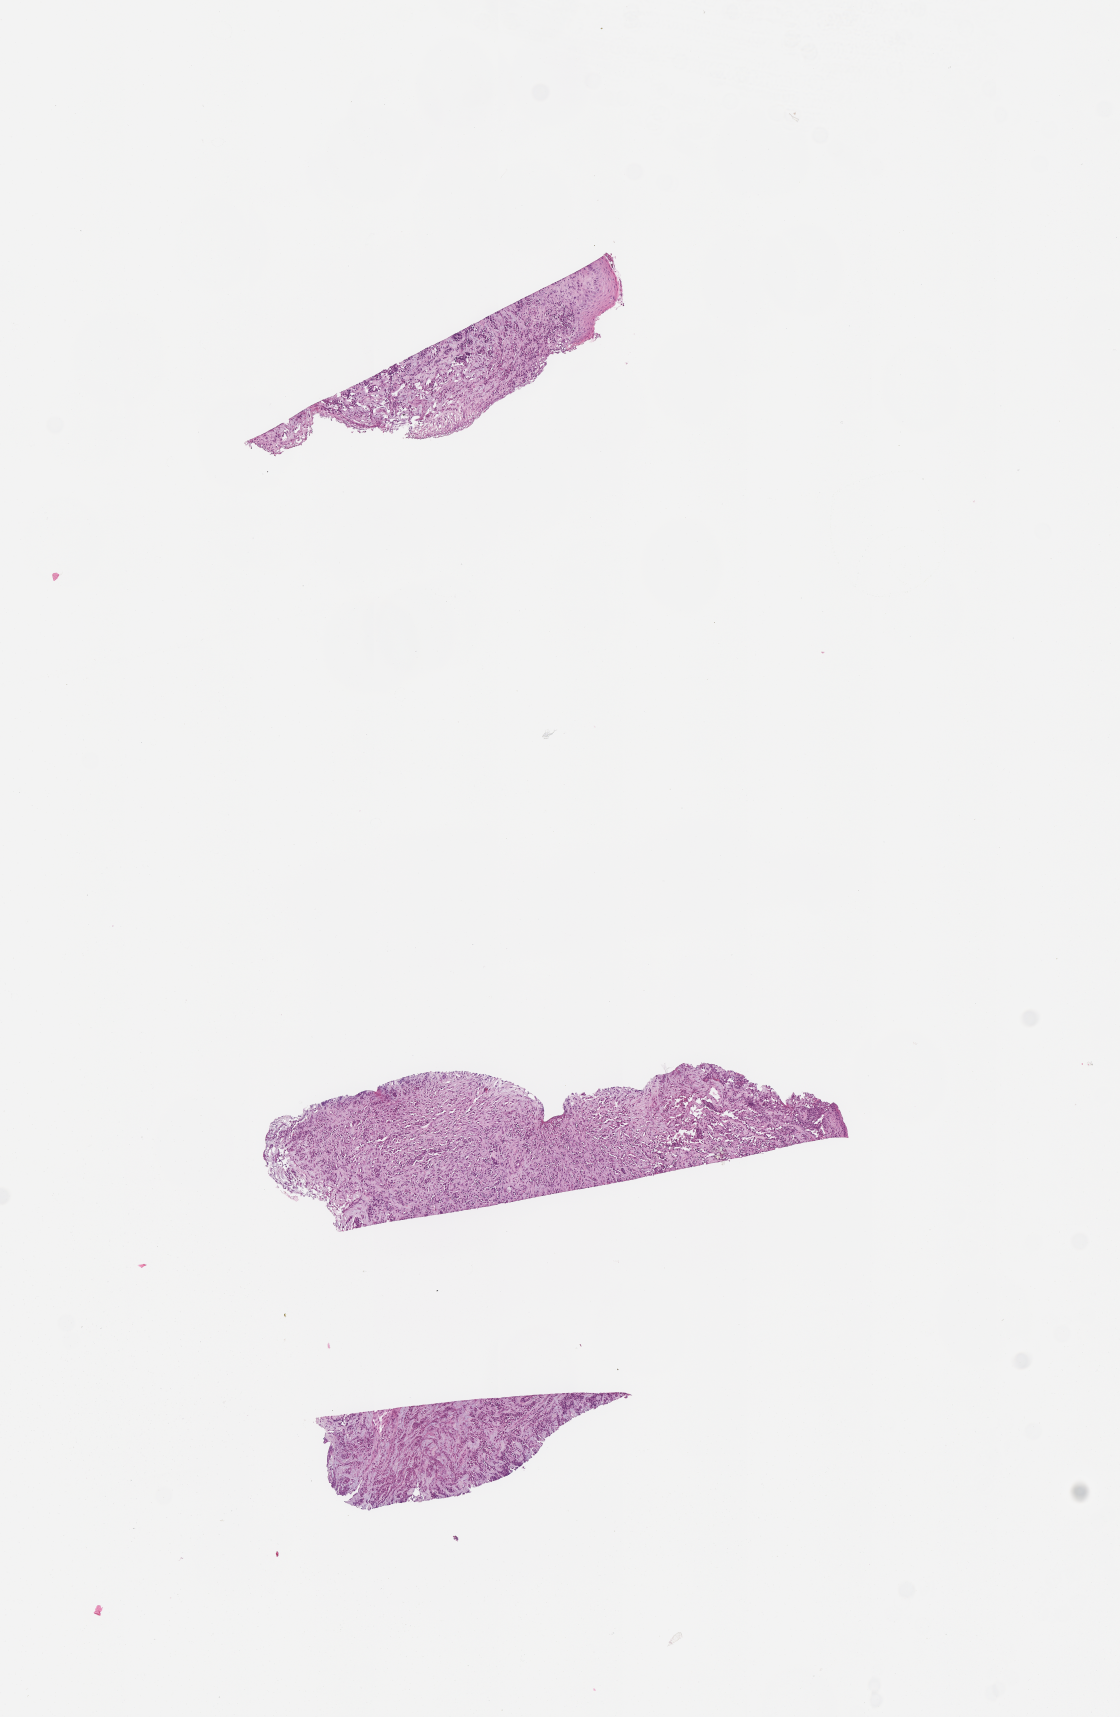
Digitized haematoxylin and eosin-stained section of tumor tissue, shown as a low-resolution overview of the whole scanned area (about 4.5 x 6.9 mm); formalin-fixed, paraffin-embedded (FFPE) tissue; site: nasal mass. Female patient, age at diagnosis 2.5 years.
Diagnosis: rhabdomyosarcoma; histological classification: alveolar rhabdomyosarcoma. Stage (as recorded): 2.